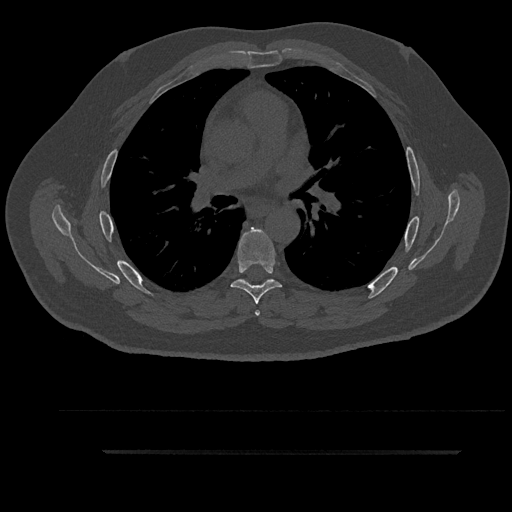
CT including the spine, one axial slice; position 580 of 797 along the scan axis; reconstruction kernel Br40s/3; bone window (W 1800 / L 400 HU); 0.5 mm slice thickness; 512 × 512 image matrix, field of view 432 × 432 mm. Male patient, age 63 years. Case-level facts recorded for this patient, not image findings: primary cancer: renal; vertebrae with lytic lesions (as recorded): T8.
Annotated regions visible in this slice (semi-automatically segmented with operator editing):
- T5 vertebra: bounding box (x1, y1, x2, y2) in pixels: (238, 279, 266, 316)
- T6 vertebra: (231, 228, 282, 304)